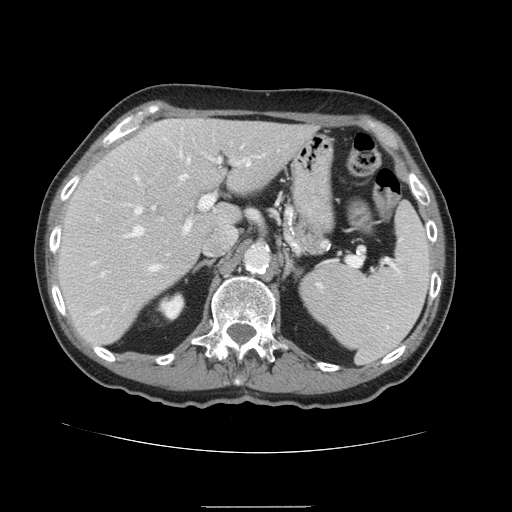
Contrast-enhanced abdominal CT, one axial slice; 120 kVp; intravenous contrast given; soft-tissue window (W 400 / L 40 HU); 2.5 mm slice thickness; 512 × 512 image matrix, field of view 386 × 386 mm. Male patient, age 74 years. From the clinical record (not read from this slice): diagnosis: colorectal cancer liver metastases, imaged before liver resection; multiple liver metastases: no; largest metastasis: 14.5 cm; disease in both lobes: yes.
Structures marked on this image (outlined manually by an expert reader):
- hepatic veins: bounding box [x1, y1, x2, y2] px = [126, 159, 250, 269]
- liver: [57, 119, 318, 345]
- planned liver remnant (the part of the liver to remain after resection): [58, 120, 317, 346]
- portal vein (with intrahepatic branches): [93, 157, 221, 236]